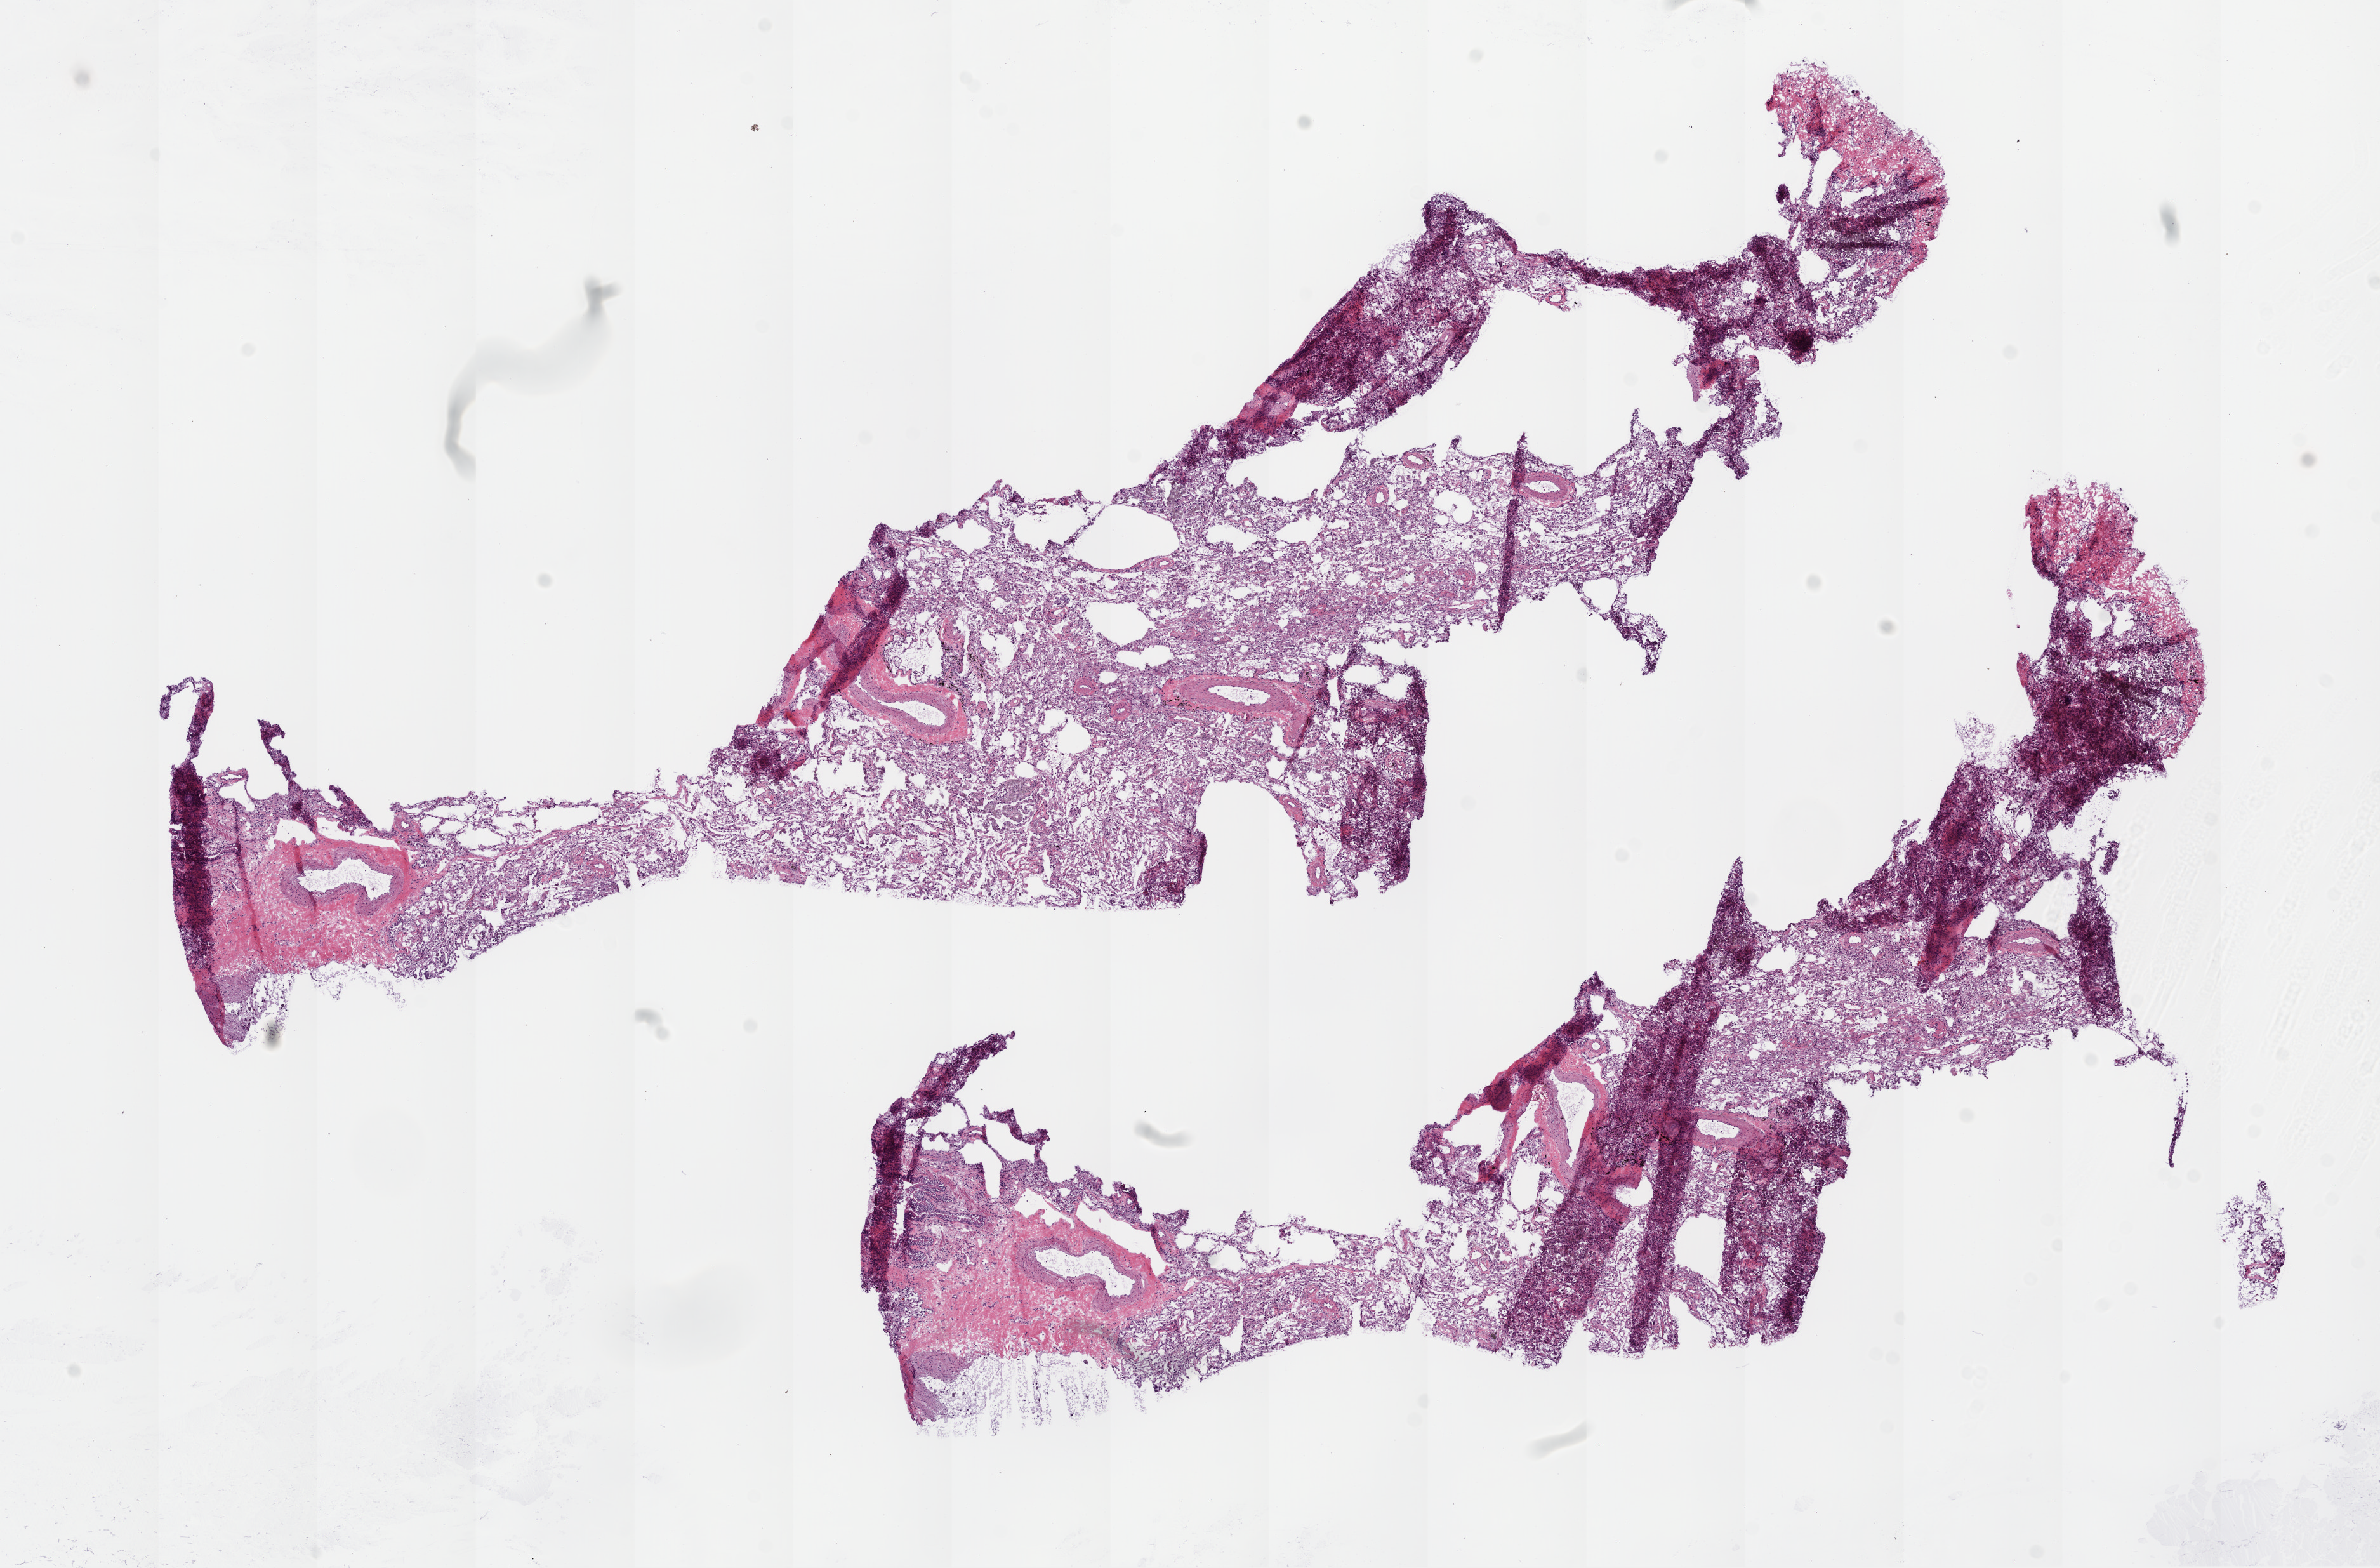
H&E-stained whole-slide image, a low-resolution overview of the entire scanned area, about 15.0 x 9.9 mm (slide scanned at 20x). Frozen section. Lung, solid tissue normal (non-tumour tissue) sample. Male patient; age at initial diagnosis 59 years.
* this section: solid tissue normal (non-tumour) sample from the same patient
* patient diagnosis: Adenocarcinoma, NOS